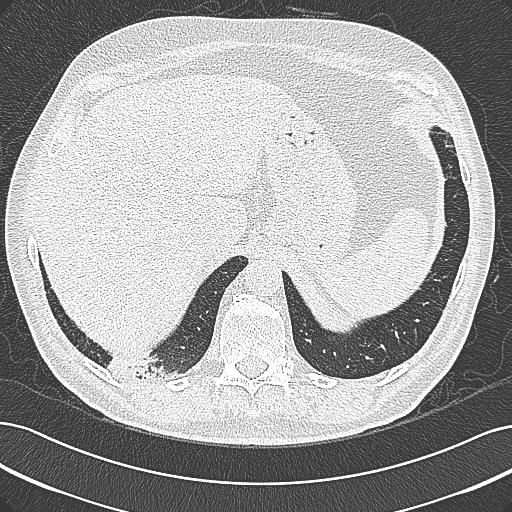
Low-dose screening chest CT, axial slice. Baseline screening round. Lung window (W 1500 / L -600 HU). Slice 260 of 355 in the series. 512 × 512 image matrix. Male participant, aged 68 years at enrolment.
Lesion marked by an expert reader, bounding box <93,336,196,396> (left, top, right, bottom; pixels). No non-calcified nodule or mass ≥4 mm was recorded by the screening reader at this exam. Participant outcome: lung cancer diagnosed 154 days after this screen — mucinous adenocarcinoma, right lower lobe, well differentiated (G1), stage IB (AJCC 6th edition), 50 mm at pathology.